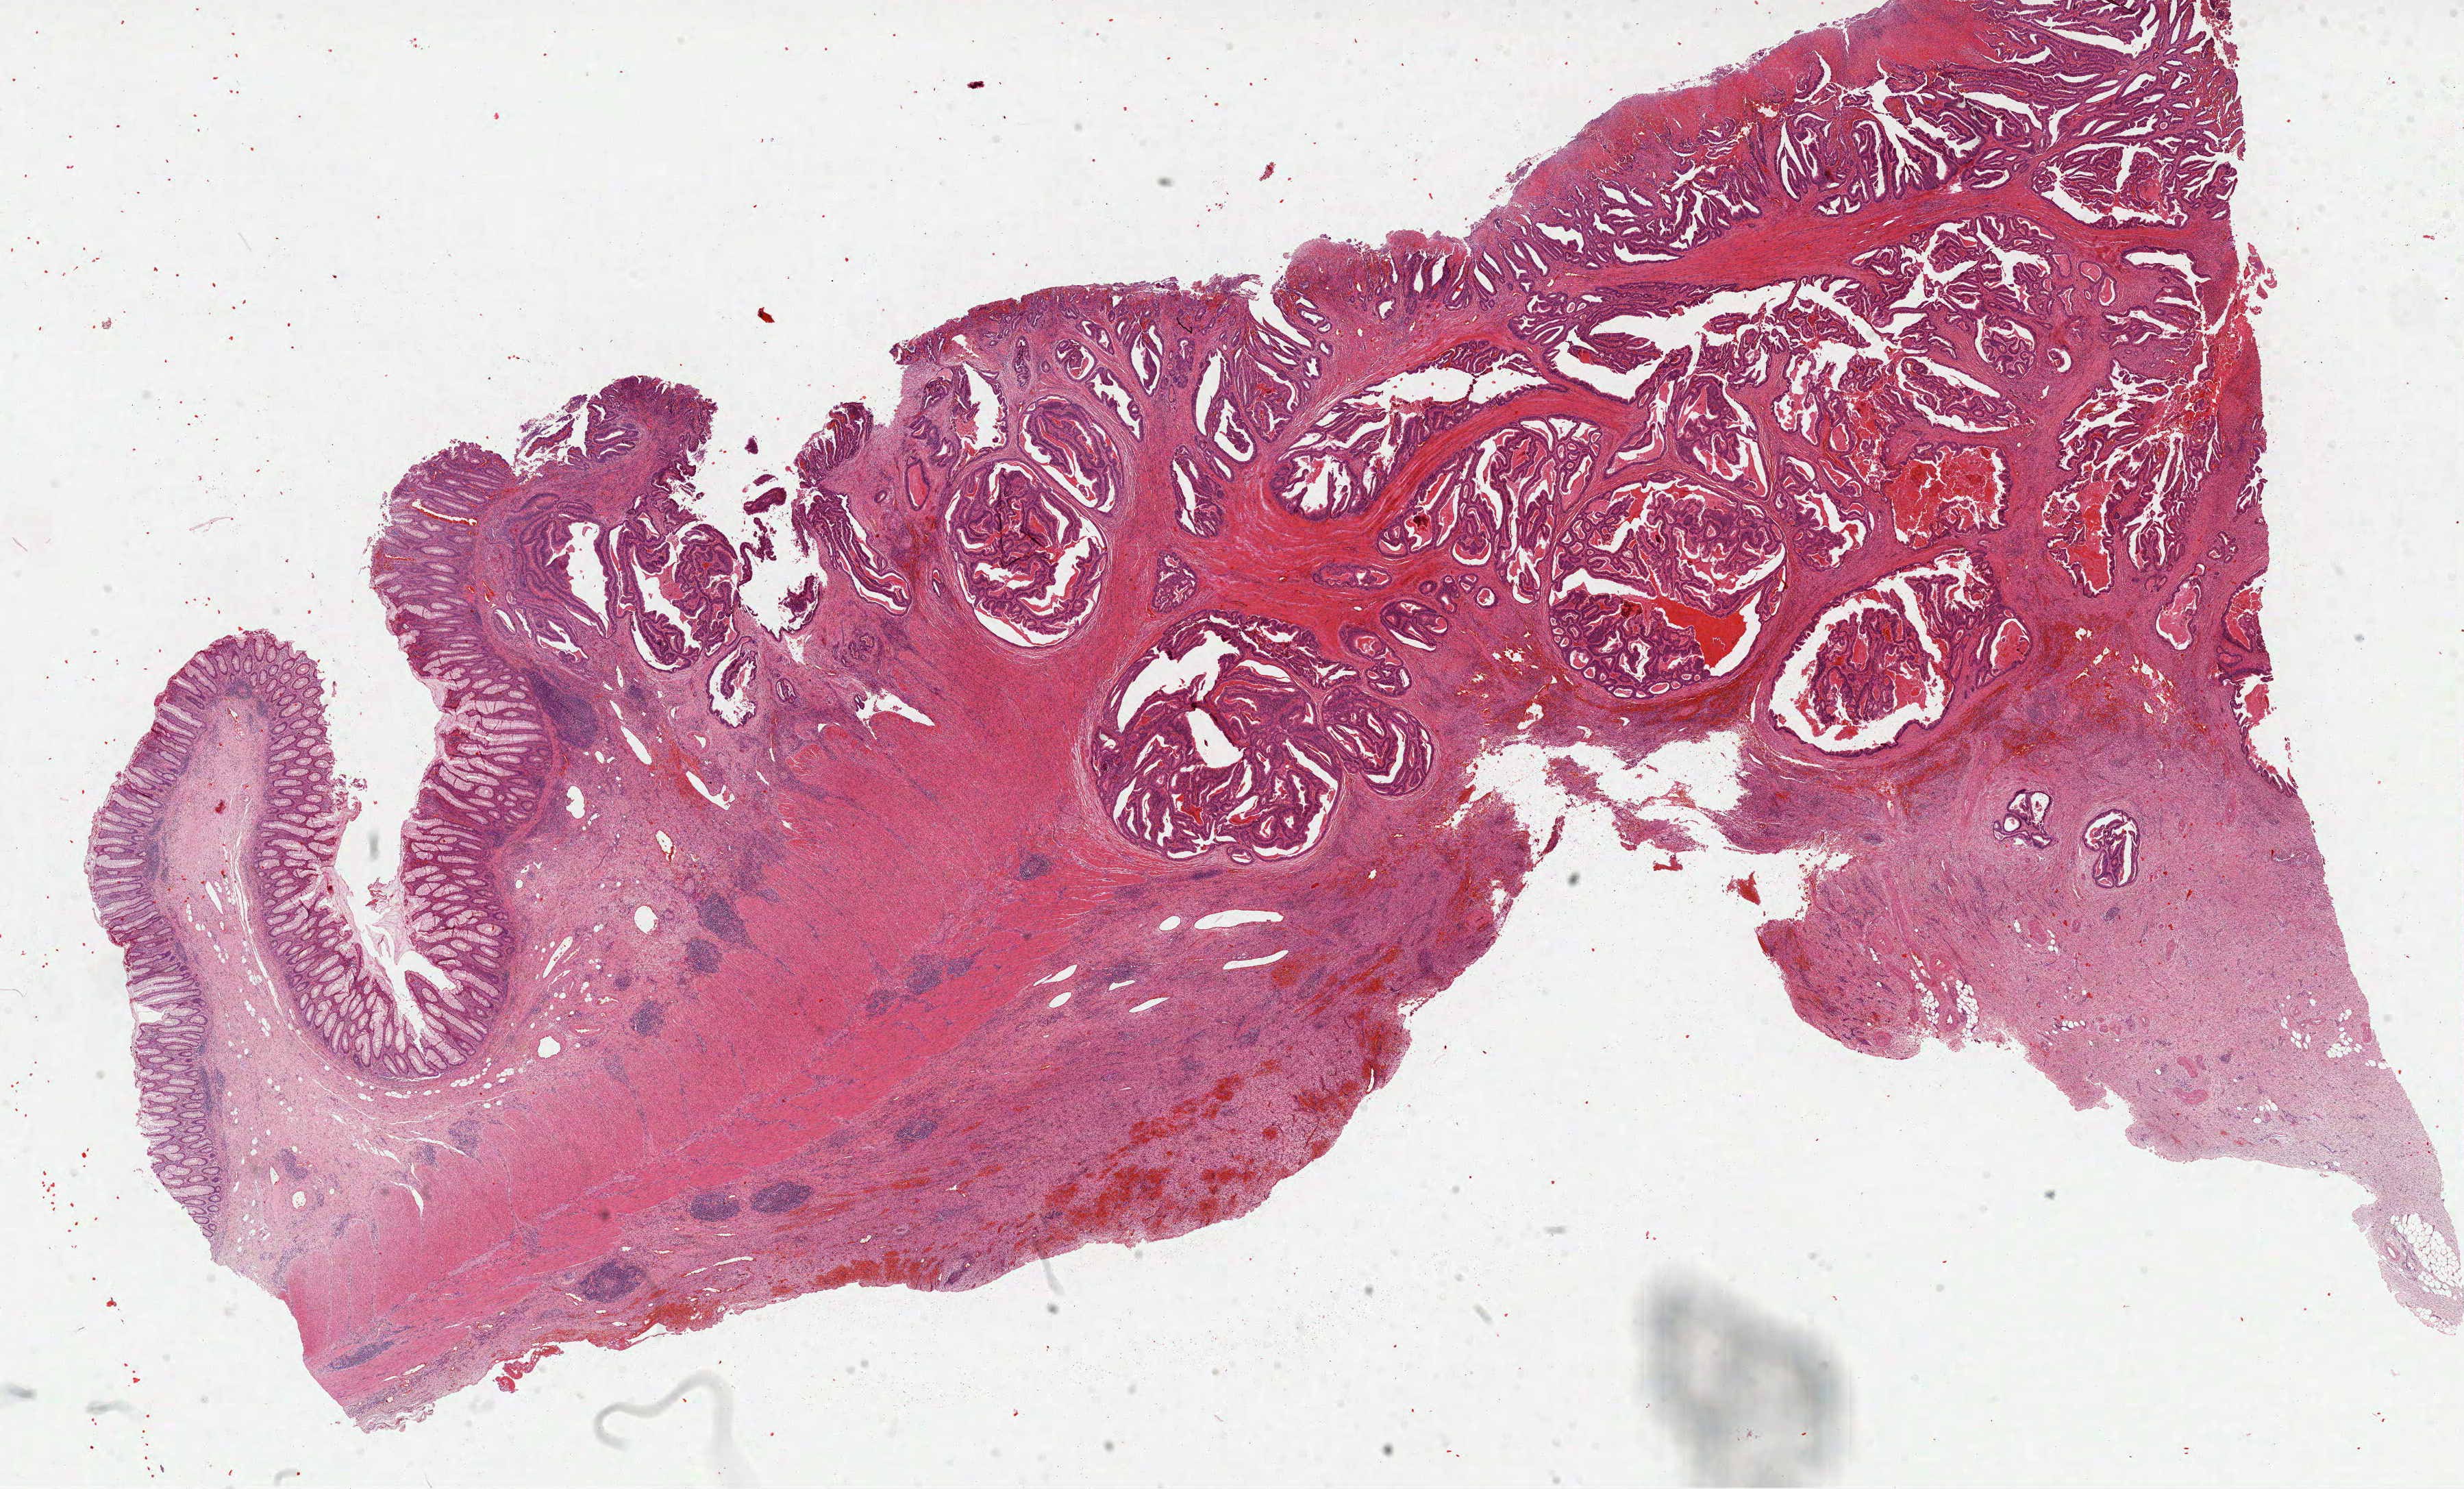
Whole-slide histology image, H&E-stained — whole scanned area (about 29.0 x 17.5 mm) shown as a low-resolution overview. FFPE section. Sample: primary tumour, rectum. Male patient; age at initial diagnosis 52 years.
AJCC pathologic stage: IIIB (7th edition). Lymph nodes positive (case pathology): 4 of 18 examined. Pathologic diagnosis: Adenocarcinoma in tubulovillous adenoma.